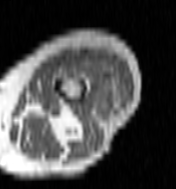
MRI of an extremity soft-tissue mass, one axial slice. Slice 31 of 100 in the series (ordered by position). MR volume resampled by the dataset authors to the PET/CT grid (not the native acquisition matrix). 176 × 189 image matrix, field of view 172 × 185 mm. Female patient. Case-level facts recorded for this patient, not image findings: histological type: undifferentiated – high grade; grade: high; site of the primary tumour: left thigh.
Outlined on this slice (expert contour drawn on MRI and transferred to this co-registered scan by the dataset authors):
- gross tumour volume including surrounding oedema: box from (x=64, y=54) to (x=122, y=110) px